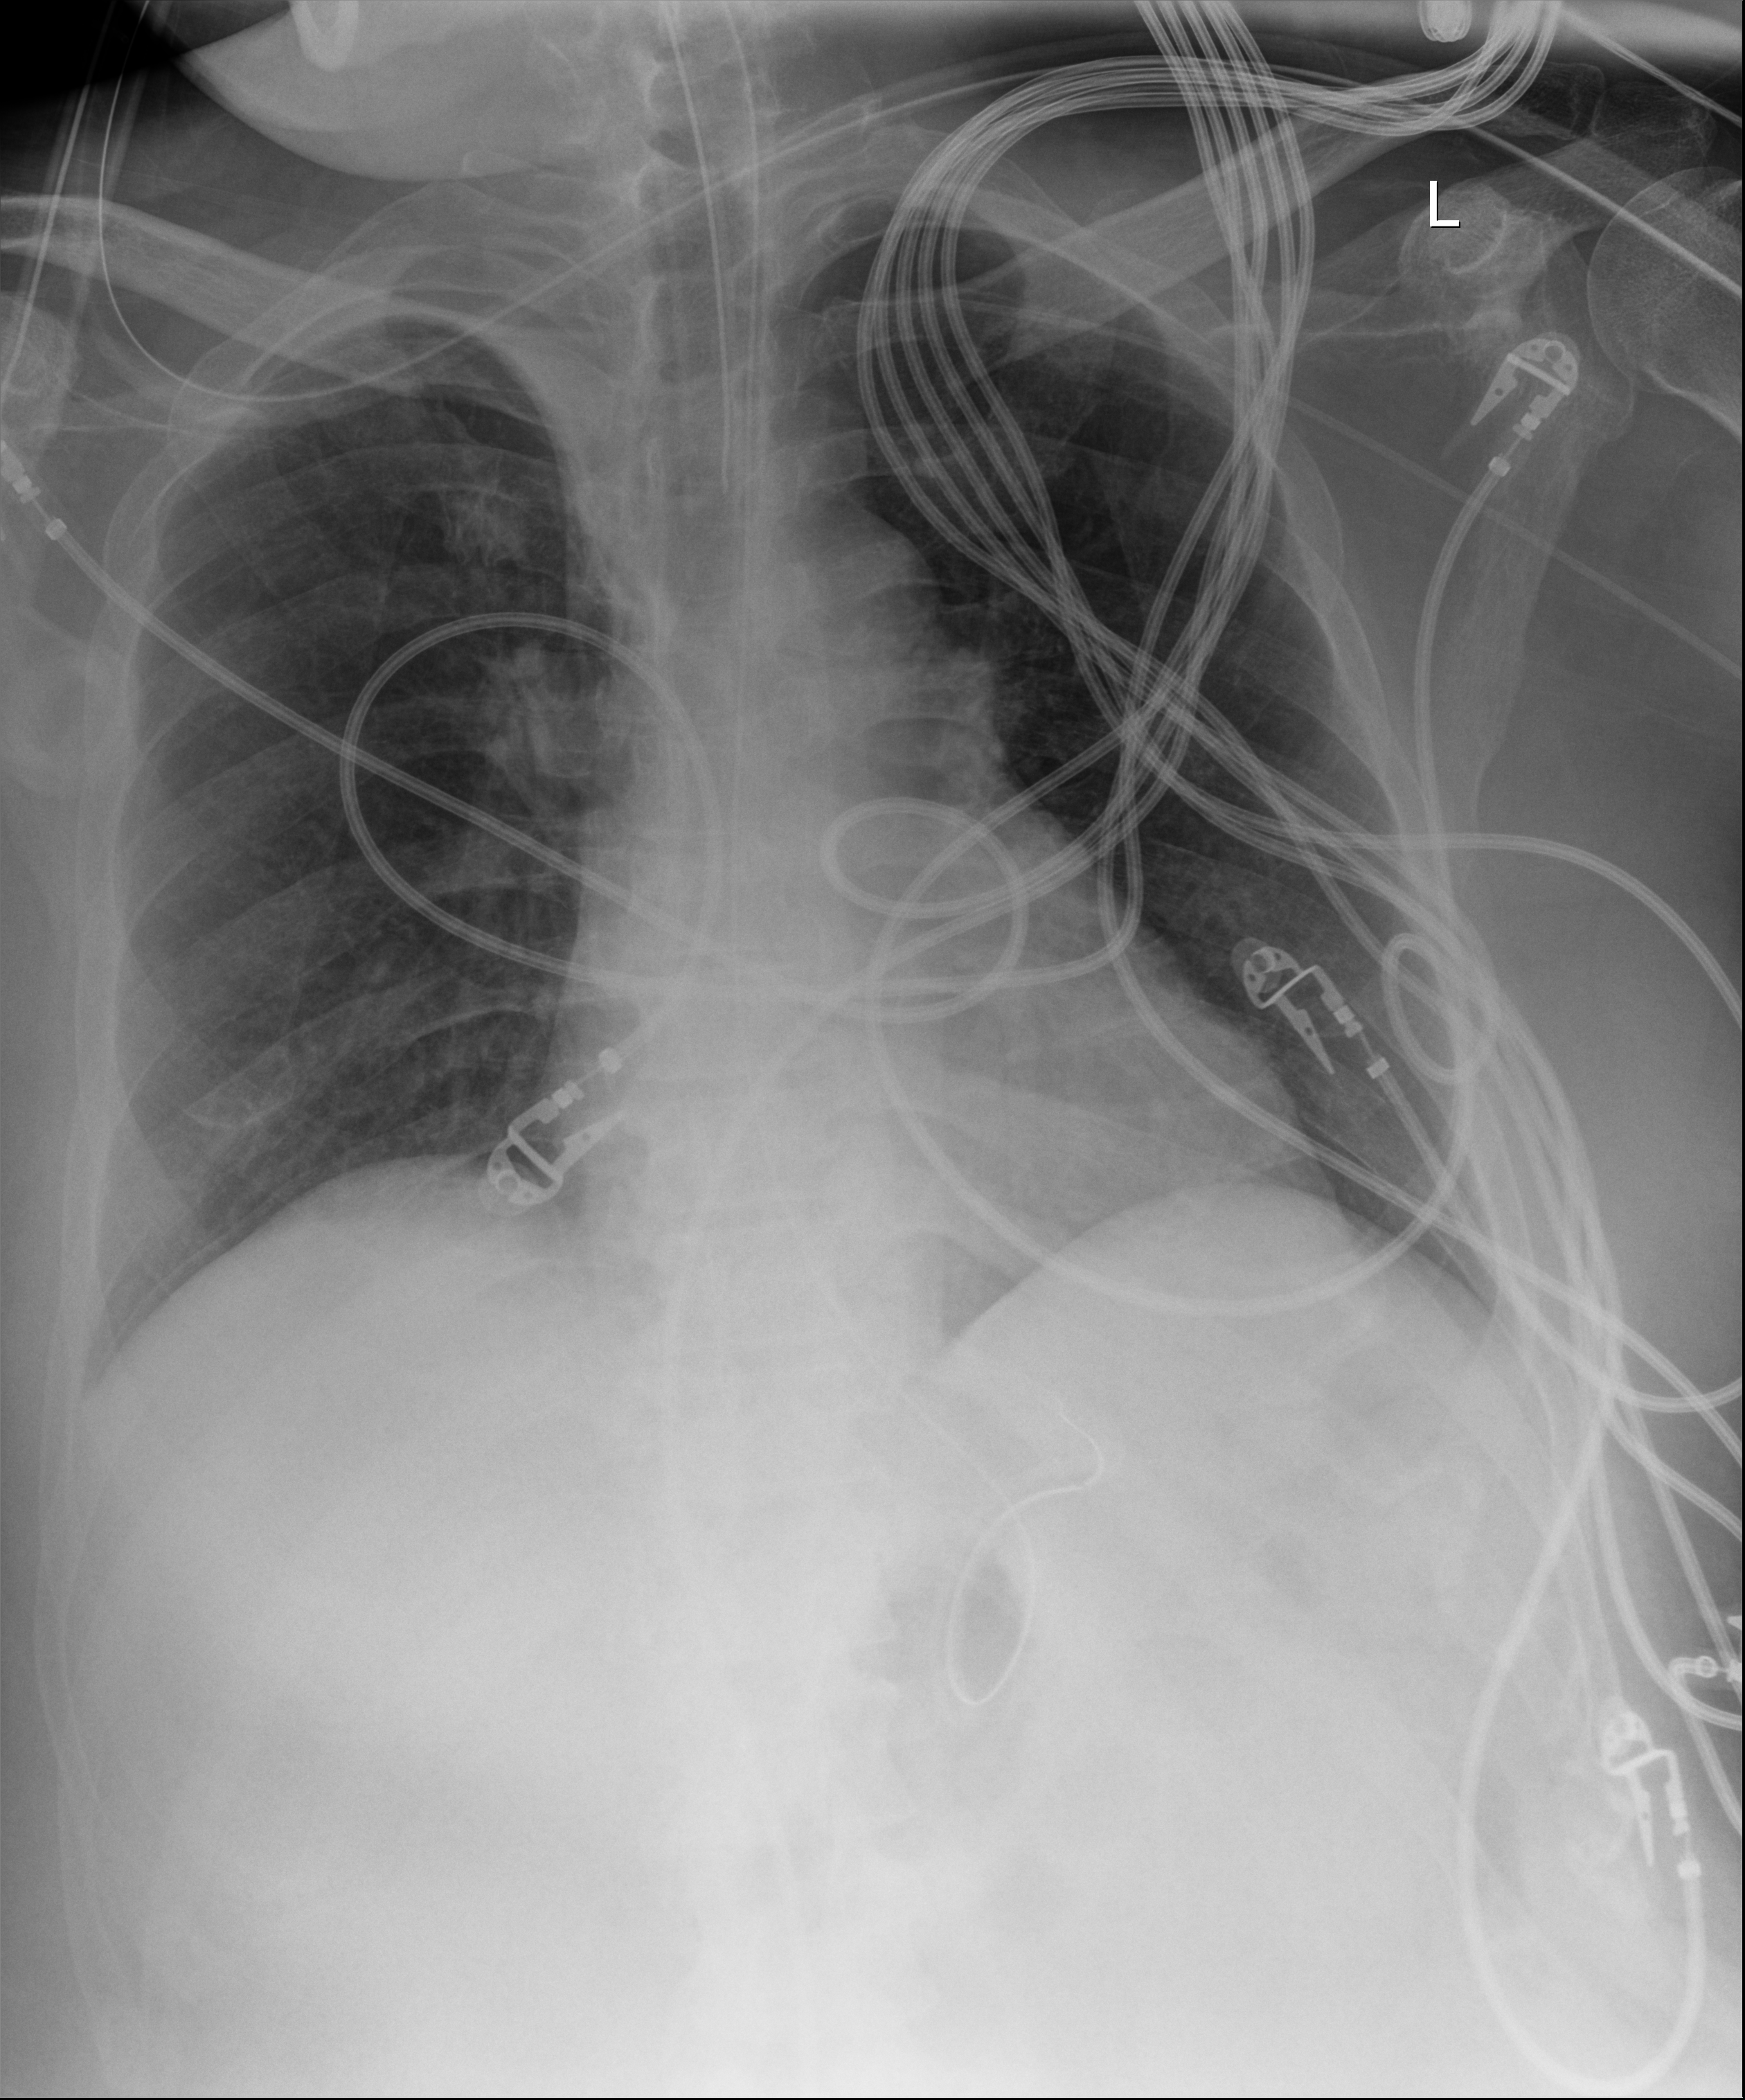
Chest X-ray (portable), anteroposterior (AP) projection. Adult patient hospitalised with COVID-19, age 18–59 years.
Hospital-stay facts (about this admission, not read from this image; timing relative to this image not recorded):
- other chronic lung disease (admission record): no
- hypertension (admission record): no
- length of hospital stay: 37 days